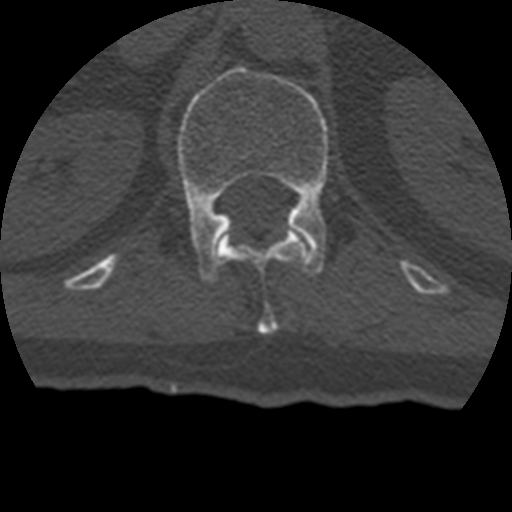
CT including the spine, one axial slice; position 157 of 399 along the scan axis; reconstruction kernel STANDARD; 120 kVp; bone window (W 1800 / L 400 HU); 1.25 mm slice thickness; 512 × 512 image matrix, field of view 160 × 160 mm. Patient age 69 years. Case-level facts recorded for this patient, not image findings: primary cancer: prostate.
Annotated regions visible in this slice (semi-automatic segmentation, software-assisted and operator-edited):
- L1 vertebra: bounding box [x1, y1, x2, y2] px = [177, 66, 329, 282]
- T12 vertebra: [217, 228, 309, 335]